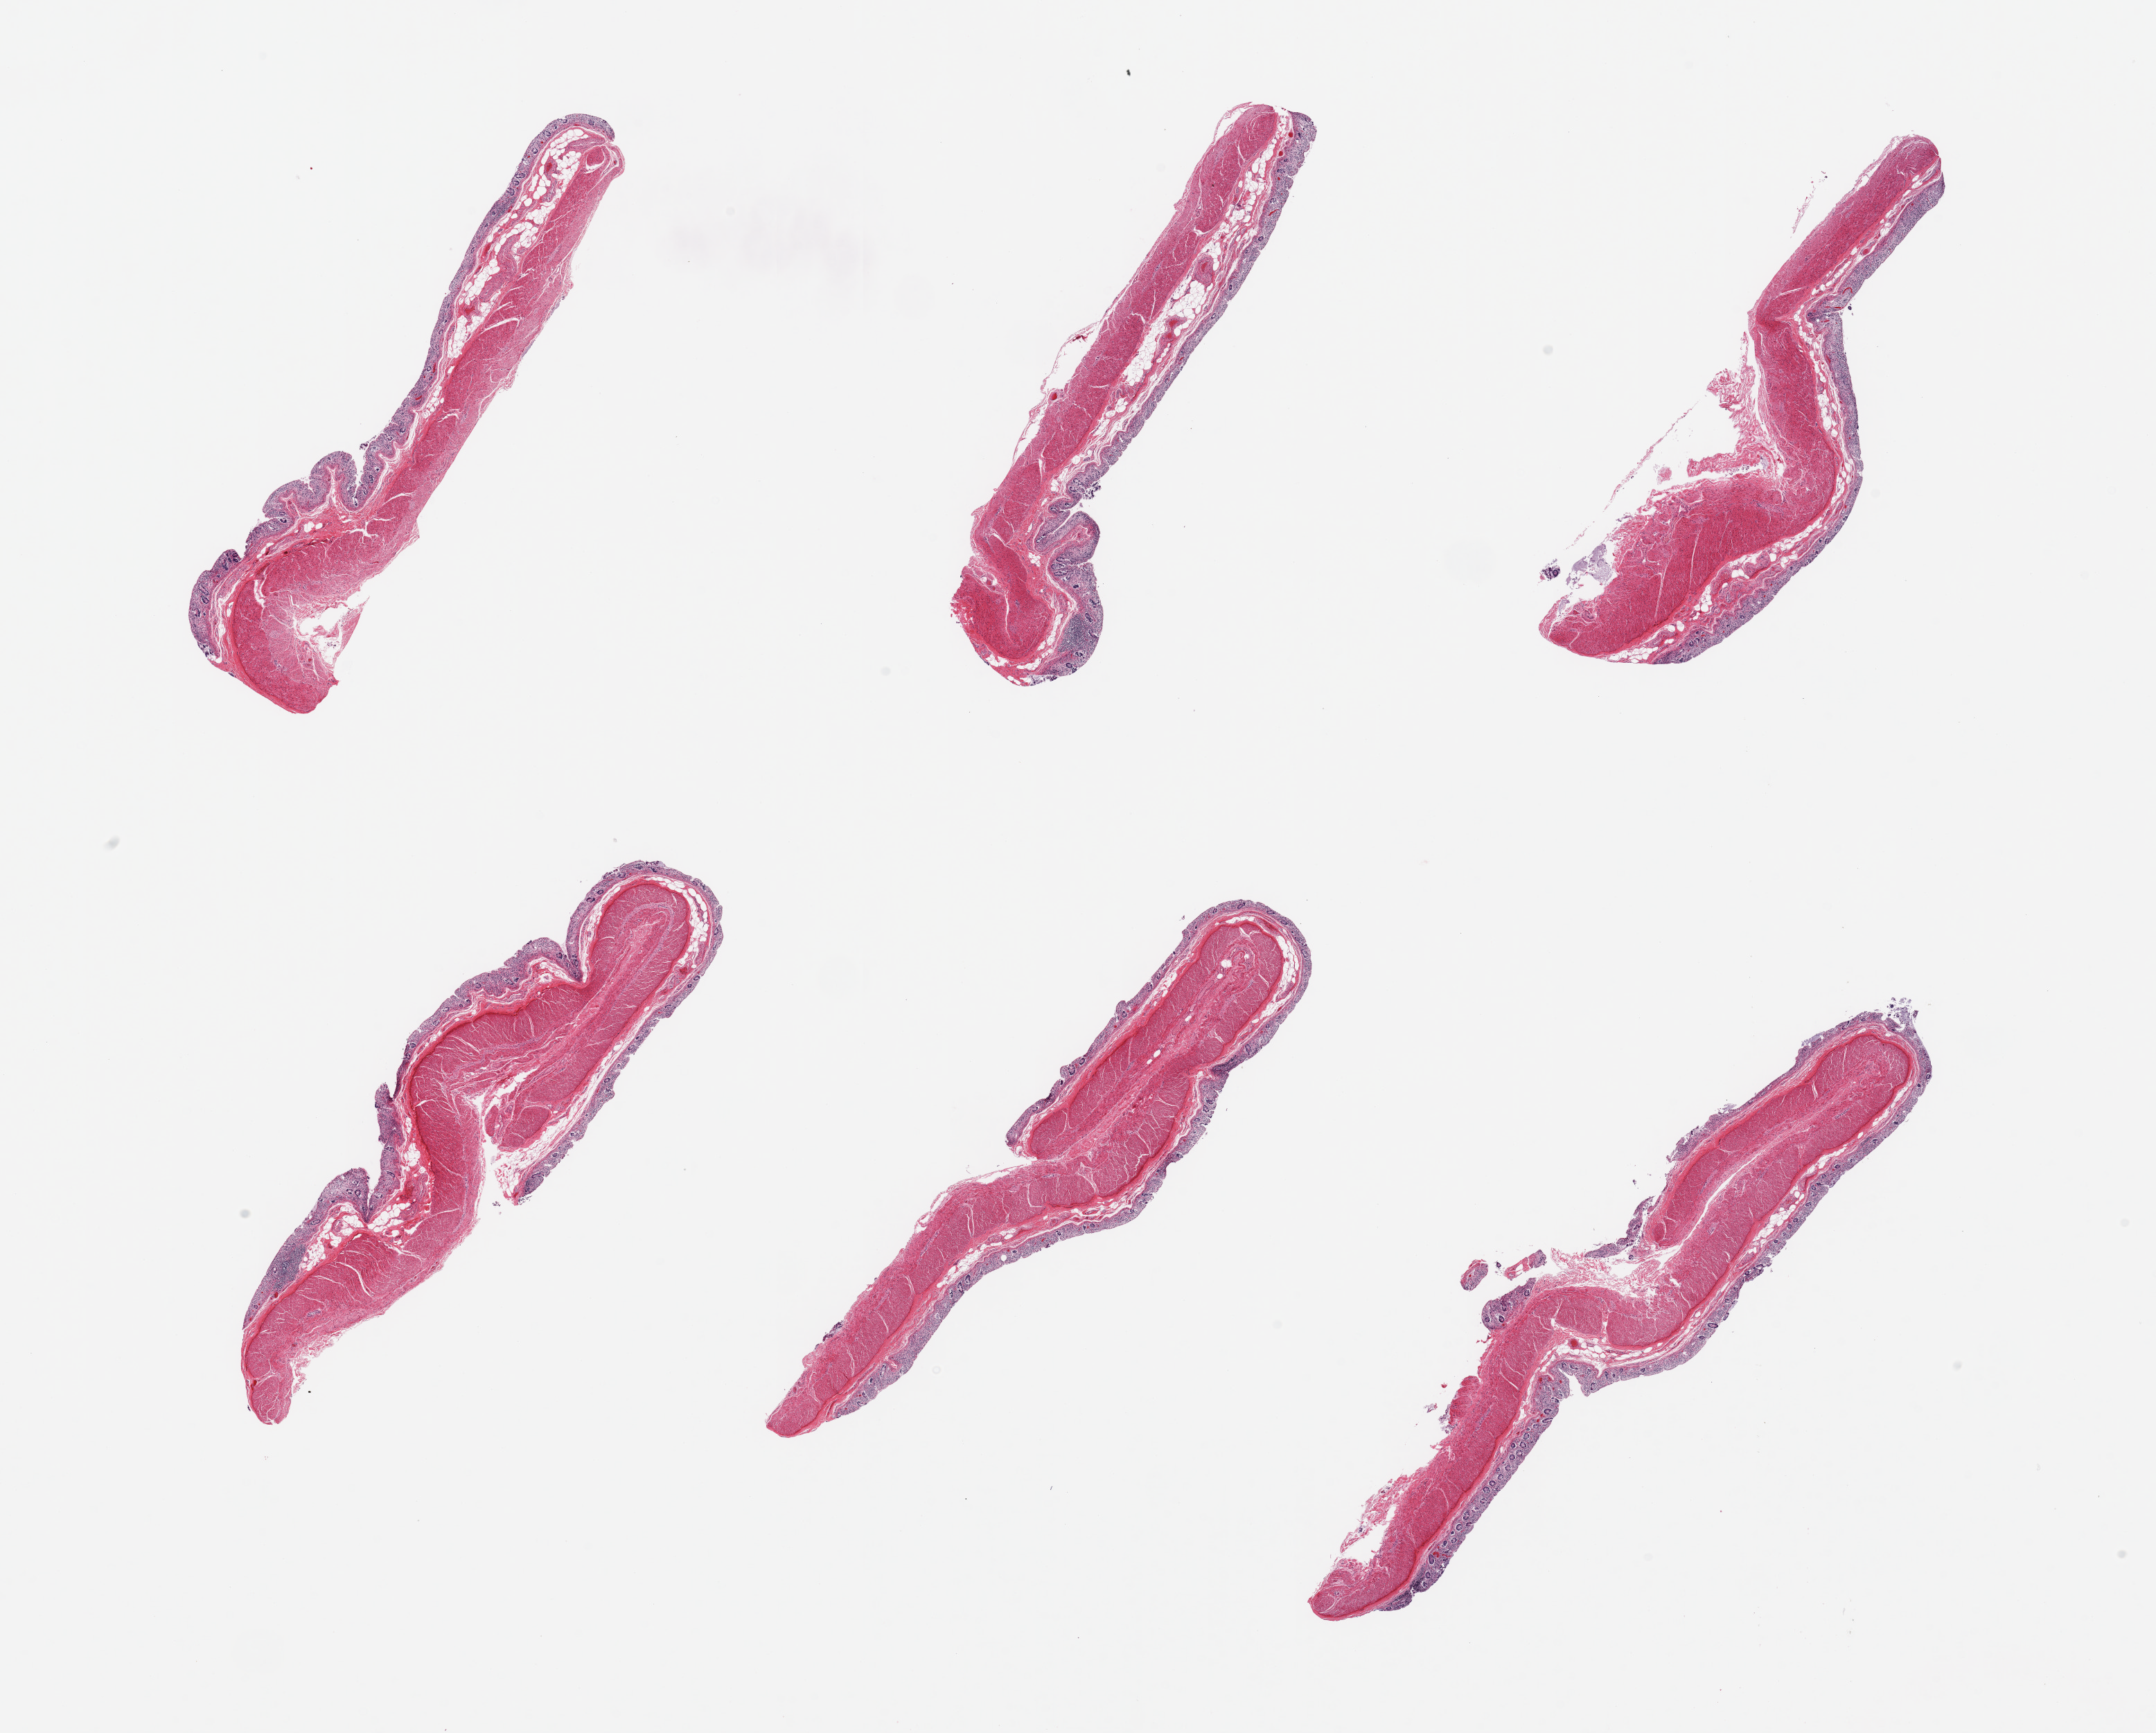
Whole-slide image, haematoxylin and eosin stain, brightfield — low-resolution overview of the scanned area, about 24.6 x 19.8 mm. PAXgene-fixed paraffin-embedded (PFPE) section. Sampled site (target tissue): transverse colon. Donor tissue sample.
Reviewer comment on this tissue sample: 6 pieces; mucosa autolyzed, muscle intact.